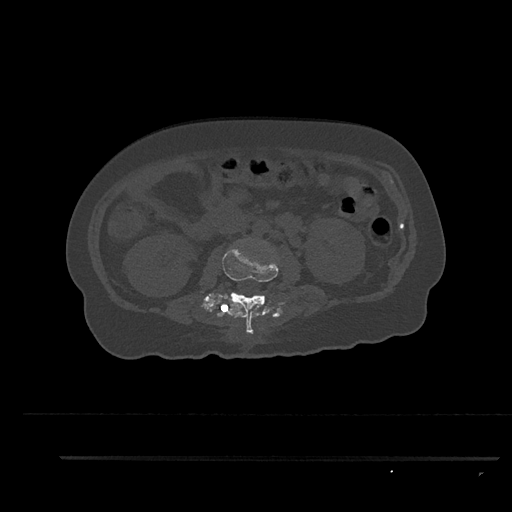
CT including the spine, one axial slice. Position 138 of 797 along the scan axis. Reconstruction kernel Br40s/3. 120 kVp. Bone window (W 1800 / L 400 HU). 0.5 mm slice thickness. 512 × 512 image matrix, field of view 408 × 408 mm. Patient: female, 44 years. From the clinical record (not read from this slice): primary cancer: renal.
Structures marked on this image (semi-automatic segmentation, software-assisted and operator-edited):
- L2 vertebra: box from (x=222, y=247) to (x=278, y=335) px